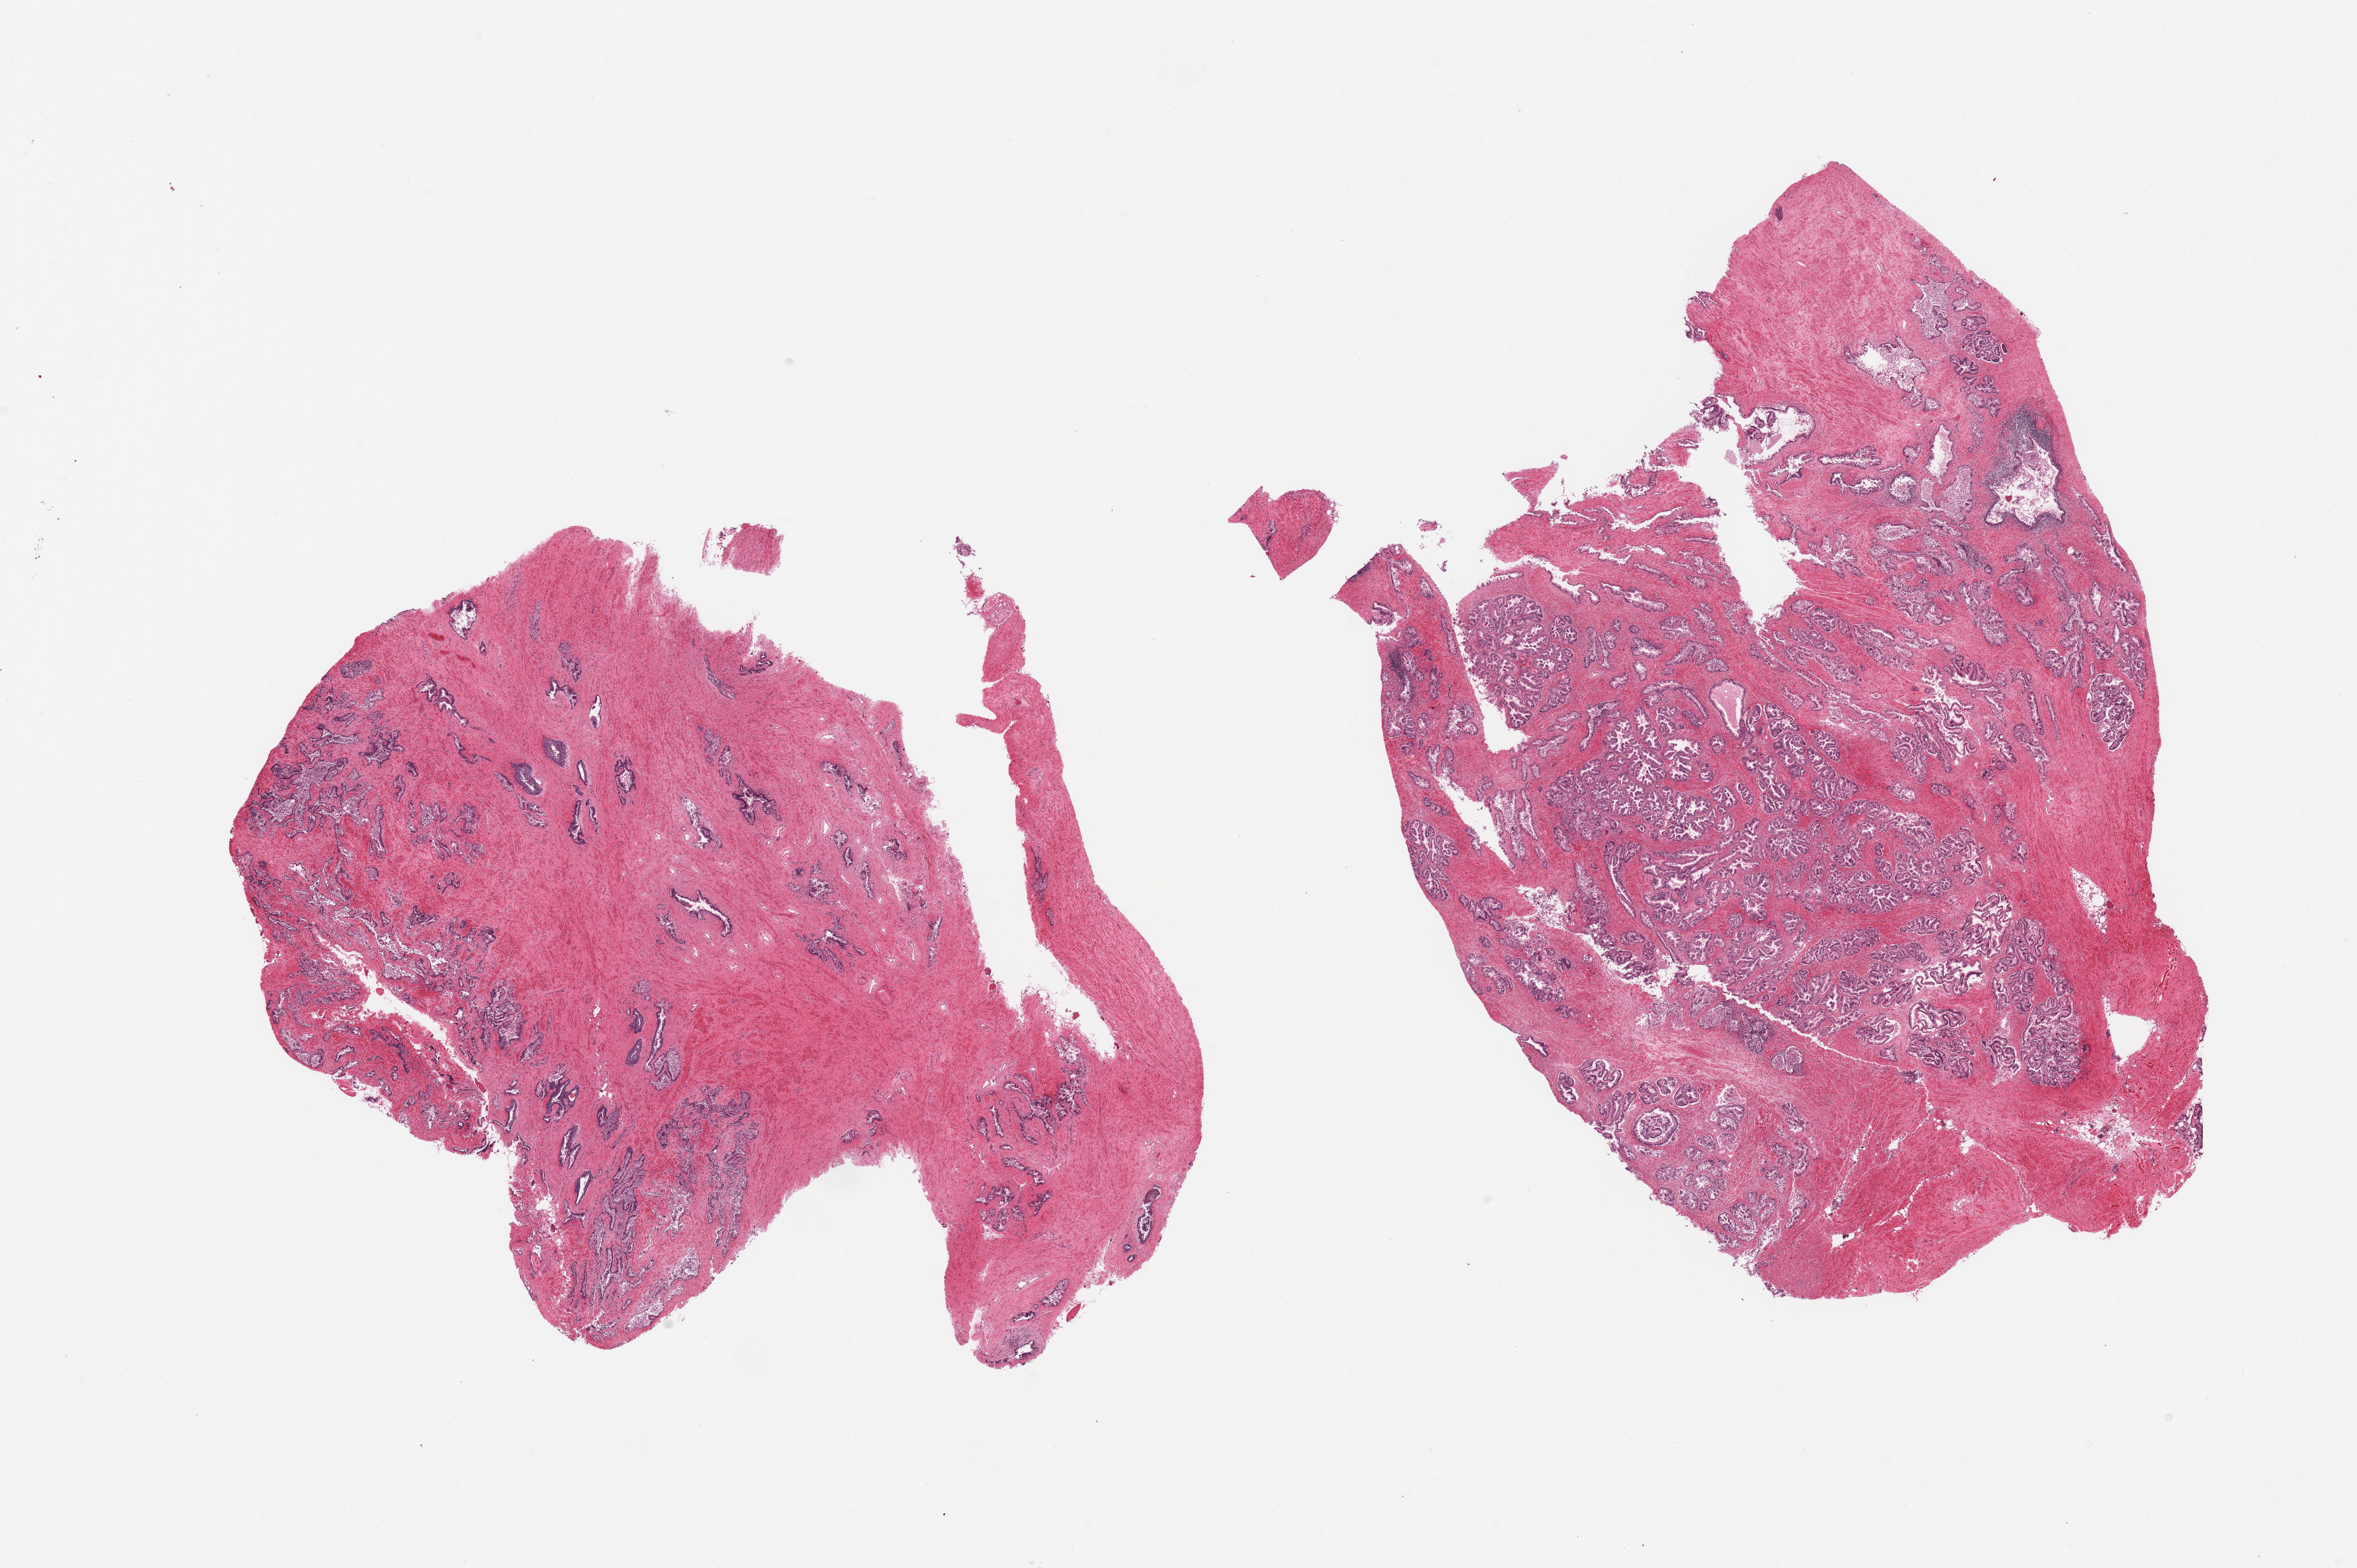
Whole-slide image, H&E stain, brightfield, a low-resolution overview of the entire scanned area, about 27.6 x 18.3 mm. PAXgene-fixed paraffin-embedded (PFPE) section. Section of prostate (target tissue). Donor tissue sample. Donor: male.
Pathologist's review note for this sample: 2 pieces, epithelium largely sloughed, glandular hyperplasia, chronic prostatitis, some basal cell hyperplasia.